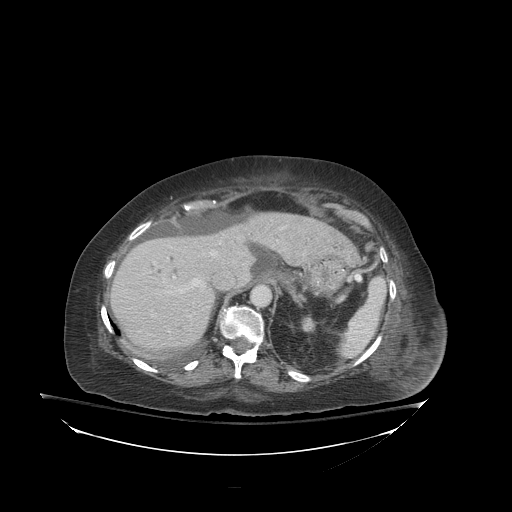
Contrast-enhanced abdominal CT (liver protocol), one axial slice. Slice 62 of 81 in the series (ordered by position). Reconstruction kernel STANDARD. Soft-tissue window (W 400 / L 40 HU). 2.5 mm slice thickness. 512 × 512 image matrix, field of view 500 × 500 mm. Case-level facts recorded for this patient, not image findings: diagnosis: hepatocellular carcinoma (patient treated with transarterial chemoembolisation; whether this scan precedes or follows treatment is not stated here); TNM stage (as recorded): Stage-I; Child-Pugh class: B; tumour nodularity: uninodular.
Outlined on this slice (semi-automatic segmentation, software-assisted and operator-edited):
- liver parenchyma outside the tumour (the mass and vessels are separate outlines, so this box may not span the whole liver): bounding box <110,212,330,352> (left, top, right, bottom; pixels)
- liver vessels: <174,252,216,293>